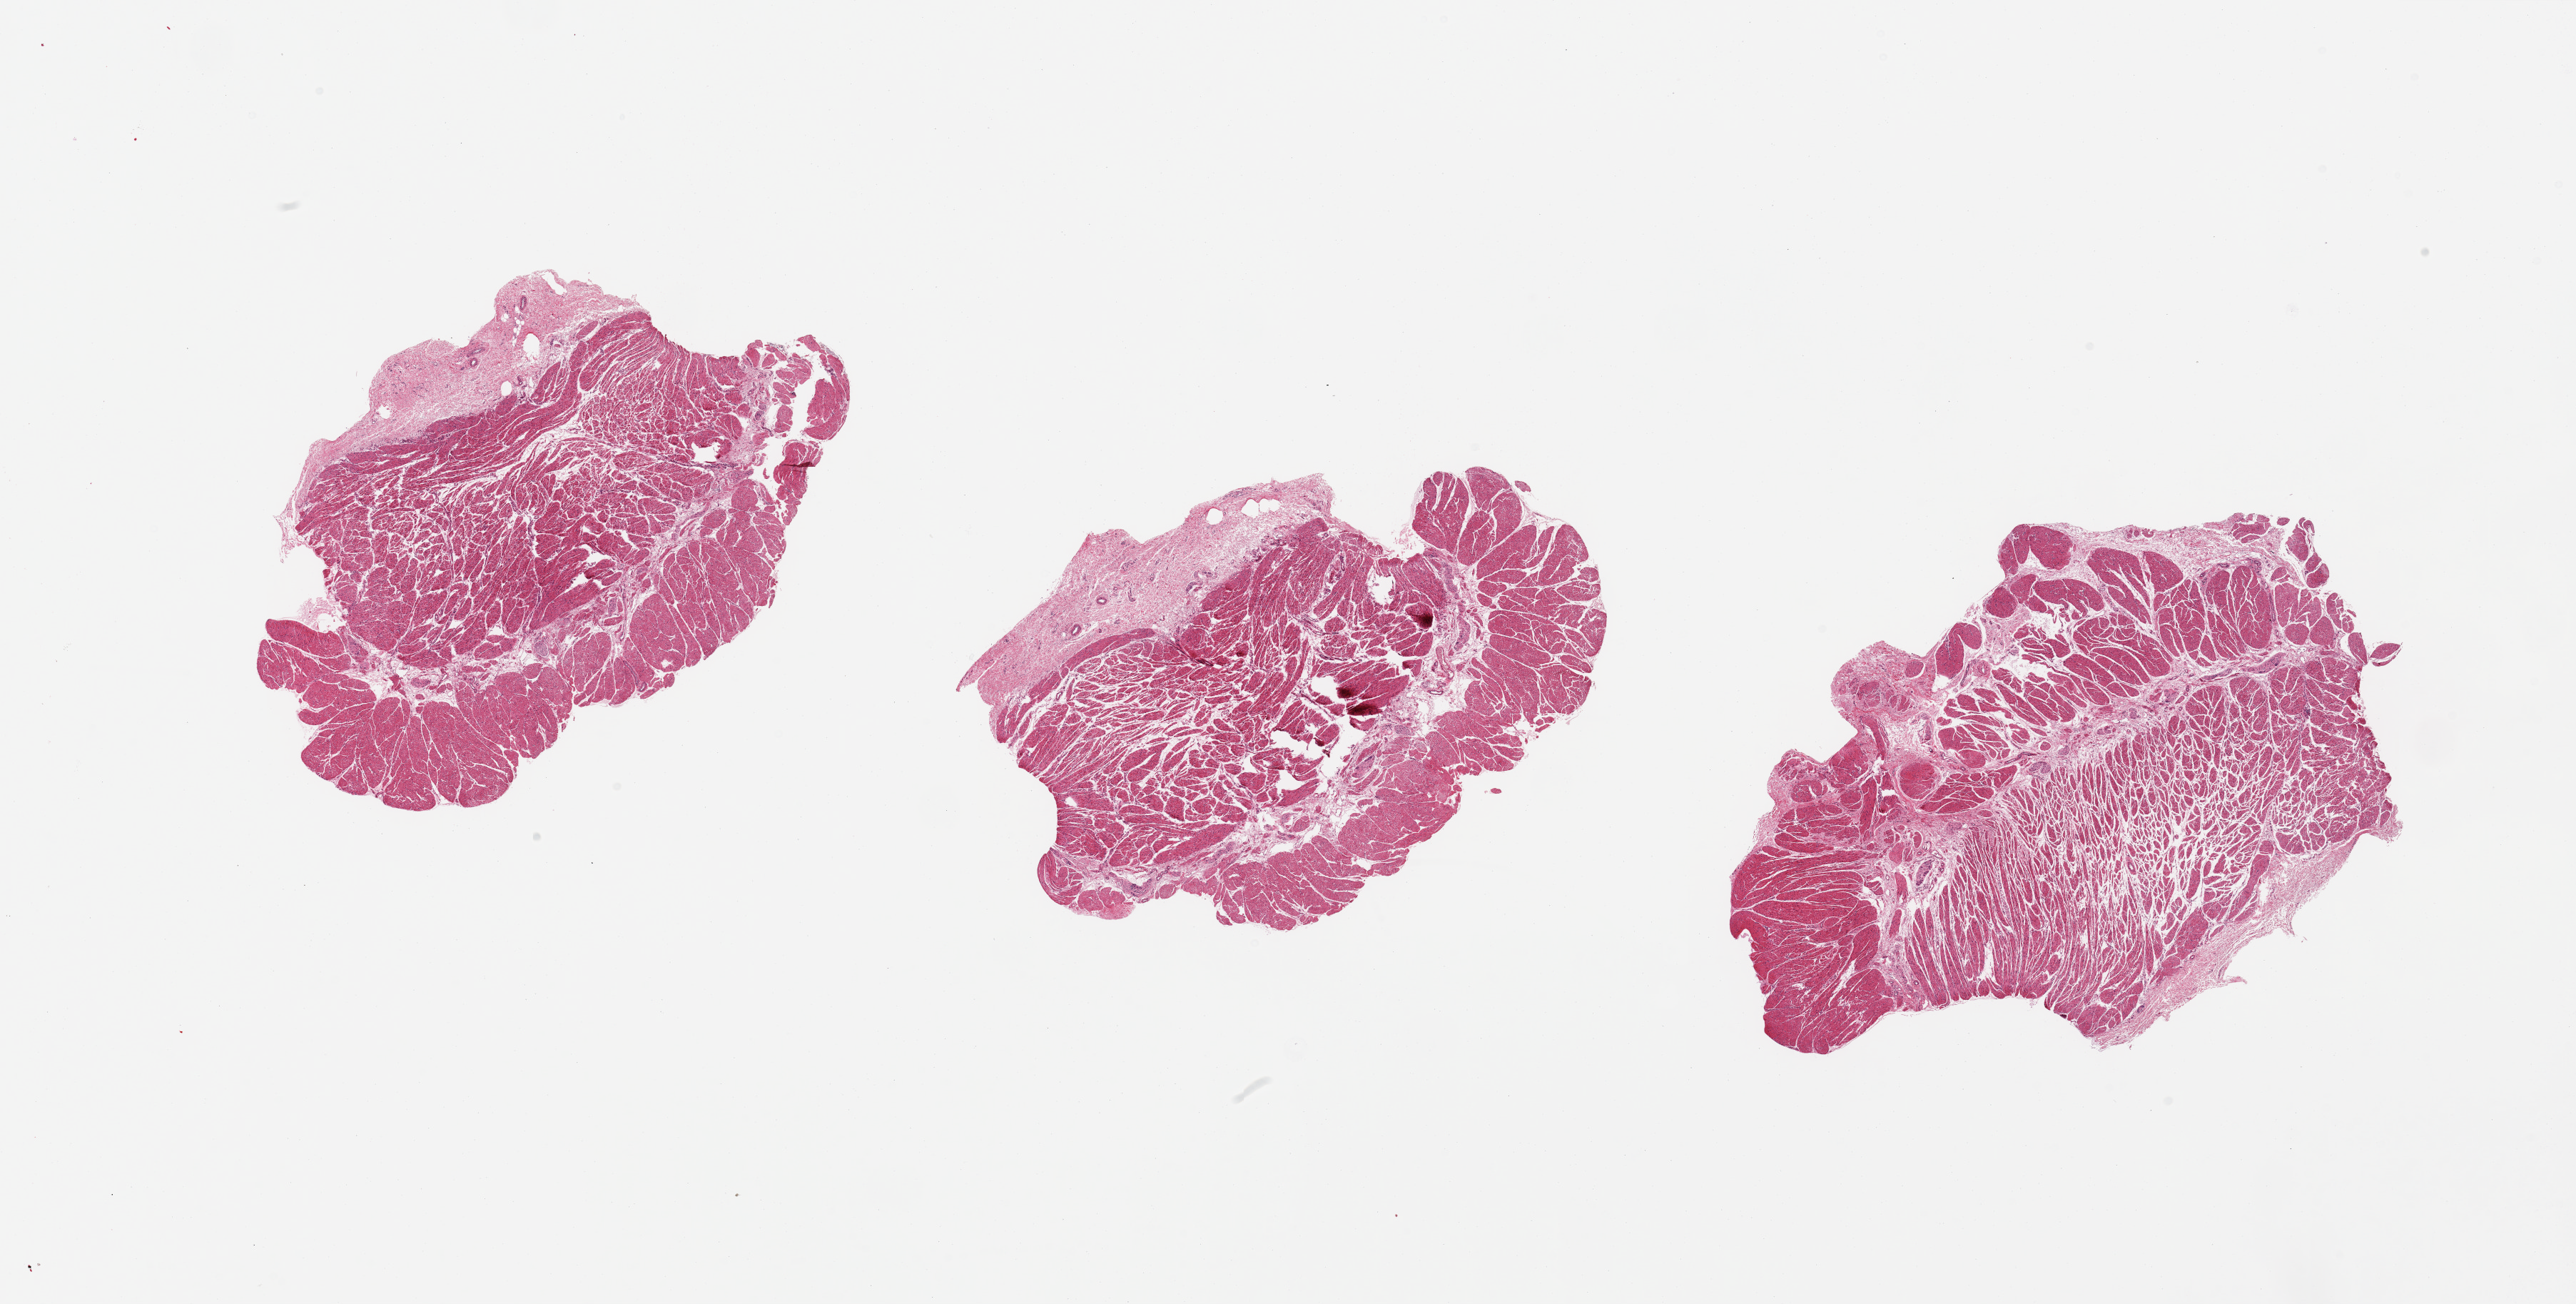
Digitized hematoxylin and eosin (H&E)-stained section, brightfield, a low-resolution overview of the entire scanned area, about 28.5 x 14.4 mm; PAXgene-fixed, paraffin-embedded tissue; section of esophageal muscle (target tissue); donor tissue sample. Donor: male.
• review note (as recorded): 3 pieces; well trimmed